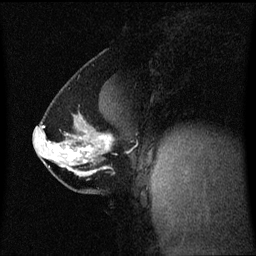
Breast MRI (dynamic contrast-enhanced), one sagittal slice; position 34 of 60 along the scan axis; dynamic contrast-enhanced series, image 2 of 3 at this slice position (ordered by acquisition); 1.5 T; TE 4.2 ms, TR 8.4 ms; 2 mm slice thickness; 256 × 256 image matrix, field of view 210 × 210 mm. Patient: female, 40 years. Case-level facts recorded for this patient, not image findings: setting: breast cancer imaged before/during neoadjuvant chemotherapy; receptor status: triple-negative.
Outlined on this slice (semi-automatic segmentation, software-assisted and operator-edited):
- analysis volume of interest (the breast-tissue region the enhancement analysis was run in; not a lesion): bounding box [x1, y1, x2, y2] px = [34, 114, 116, 188]
- tumour enhancement mask (voxels above the 70 % enhancement threshold inside the analysis volume of interest): [51, 136, 112, 160]